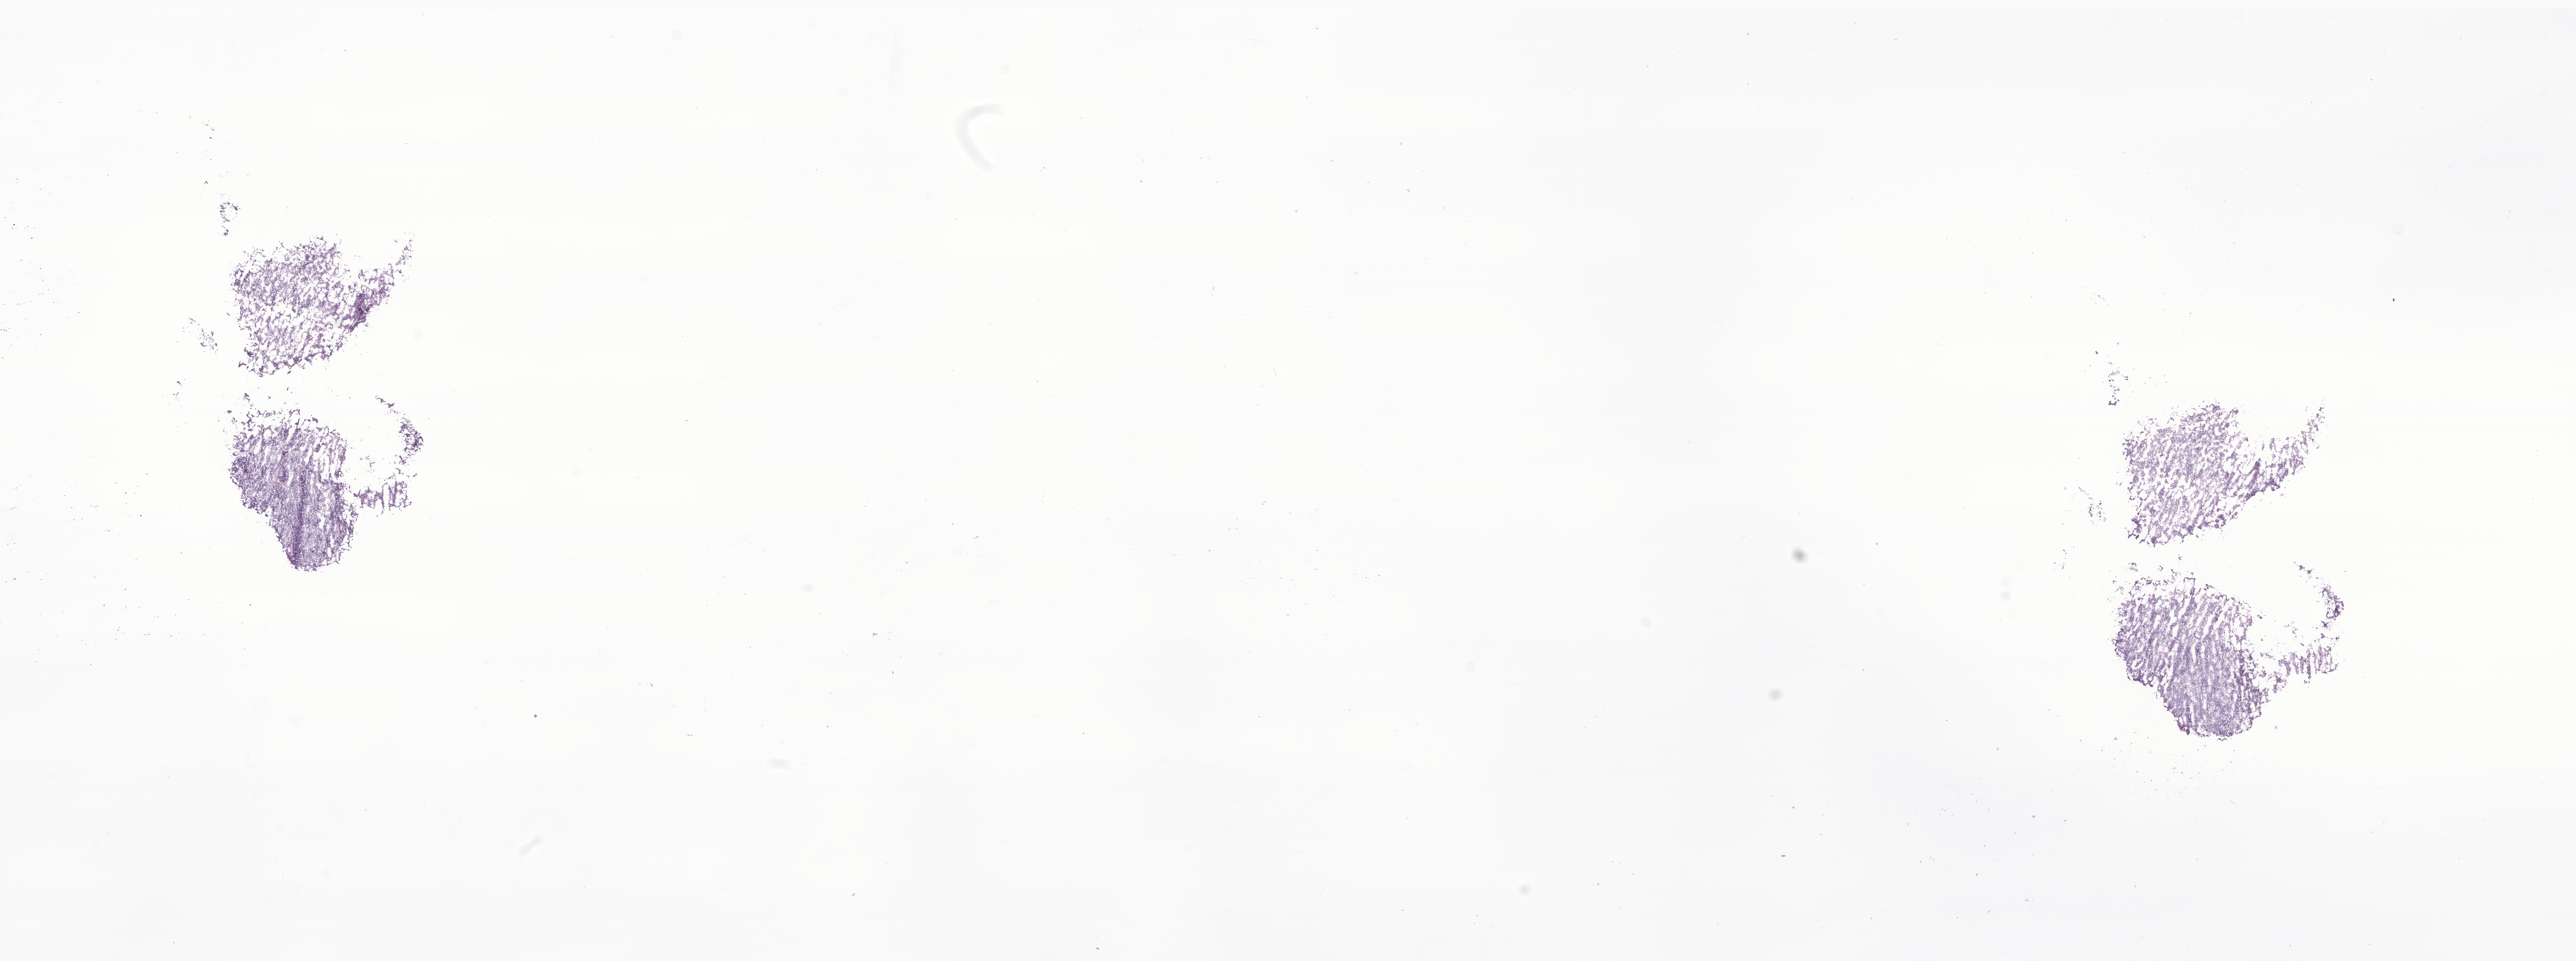
Whole-slide image, hematoxylin and eosin (H&E) stain of tumor tissue from the brain, a low-resolution overview of the entire scanned area, about 21.9 x 8.2 mm, cryosection (OCT / tissue freezing medium). Patient: female, age 38 months (3 years 2 months).
- diagnosis: Neoplasm, malignant